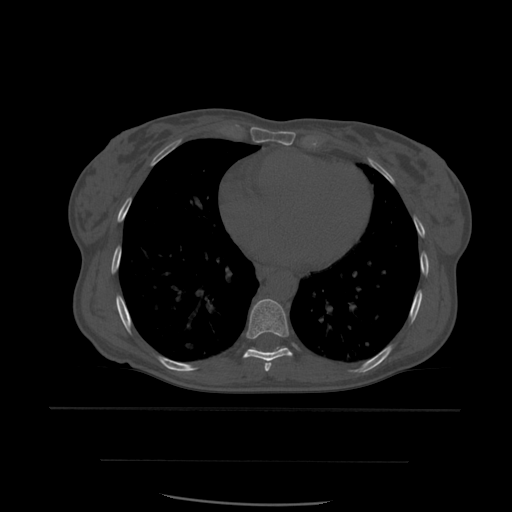
CT including the spine, one axial slice; bone window (W 1800 / L 400 HU); 512 × 512 image matrix, field of view 392 × 392 mm. Patient age 48 years. From the clinical record (not read from this slice): primary cancer: lung; vertebrae with lytic lesions (as recorded): T11.
Outlined on this slice (semi-automatic segmentation, software-assisted and operator-edited):
- T7 vertebra: bounding box [x1, y1, x2, y2] px = [265, 363, 271, 372]
- T8 vertebra: [243, 299, 293, 371]
- T9 vertebra: [249, 347, 283, 351]